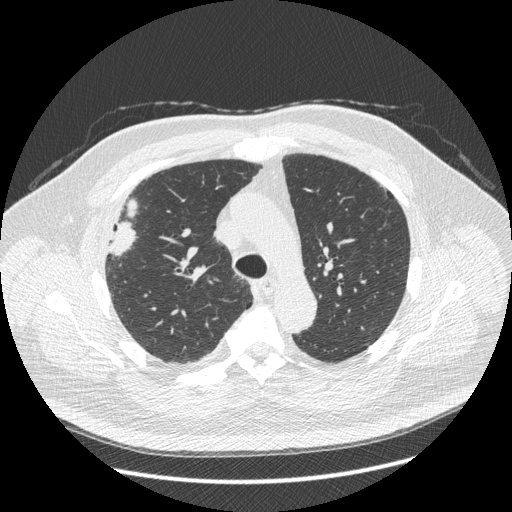
Axial slice from a low-dose chest CT screening exam. Third annual screen. Lung window (W 1500 / L -600 HU). 1.25 mm slice thickness. Standard (soft-tissue) reconstruction kernel (STANDARD). Slice 124 of 426 in the series. Male participant, aged 66 years at enrolment. Current smoker at enrolment.
Lesion marked by an expert reader, bounding box [x1, y1, x2, y2] px = [87, 202, 147, 269]. Reader record for this screening exam (exam-level; its link to the box is not recorded): non-calcified nodule or mass ≥4 mm, right upper lobe, 48 × 25 mm, spiculated (stellate) margins, soft tissue attenuation, pre-existing on the prior screen: no. Official screen result: positive, other. Participant outcome: lung cancer diagnosed 35 days after this screen — non-small cell carcinoma, right upper lobe, stage IV (AJCC 6th edition), 50 mm at pathology.